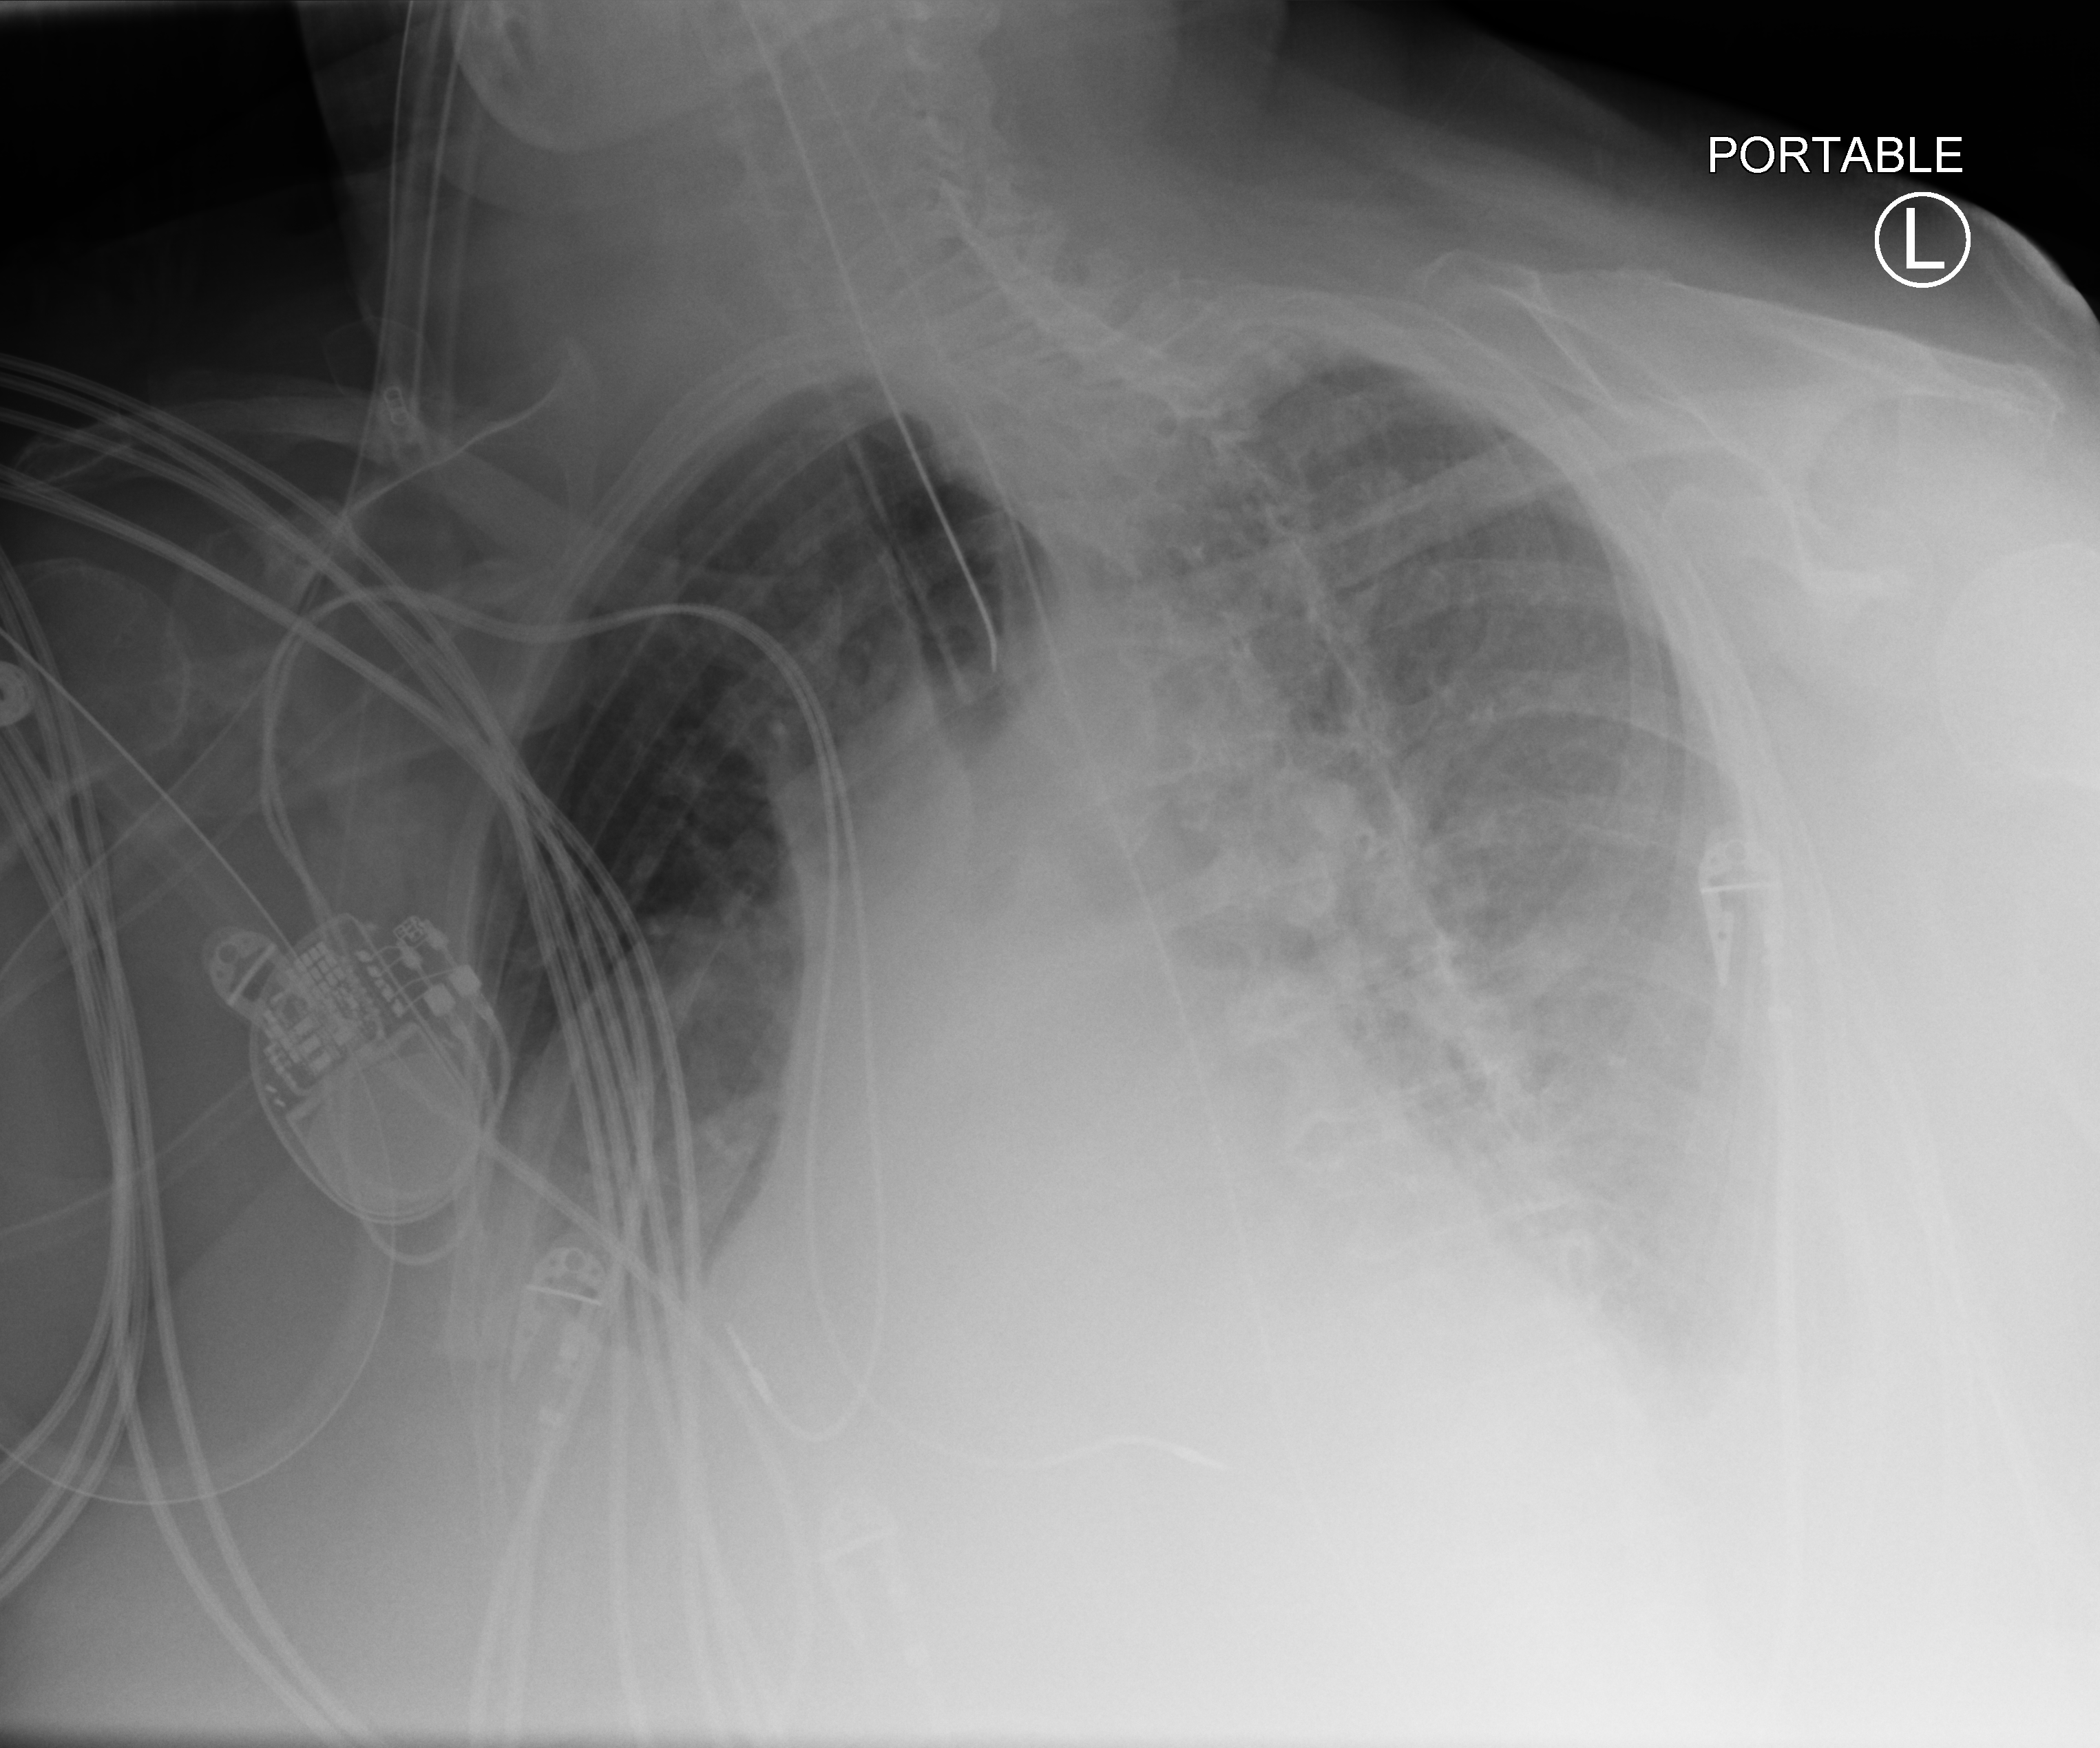
Bedside chest radiograph (computed radiography), anteroposterior (AP) projection. Female patient hospitalised with COVID-19, age 75–90 years.
From the hospital-stay record, not from the radiograph (when in the stay this image was taken is not recorded):
- COPD (admission record): yes
- admitted to intensive care during this hospital stay: yes